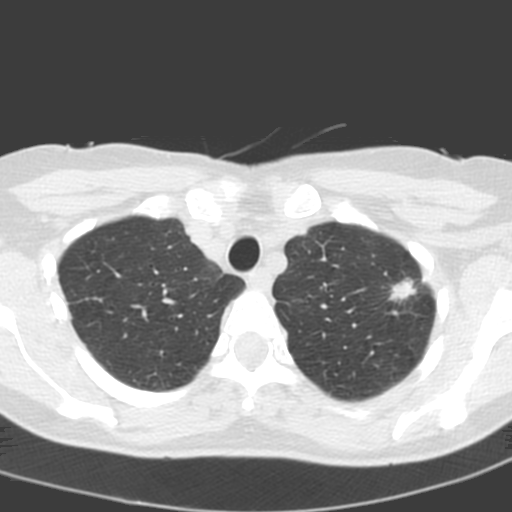
Low-dose screening chest CT, one axial slice; slice 160 of 193 in the series (ordered by position); 120 kVp; lung window (W 1500 / L -600 HU); 512 × 512 image matrix.
Outlined on this slice (outlined manually by an expert reader):
- lesion 1 (tumor, upper lobe of left lung): bounding box (x1, y1, x2, y2) in pixels: (389, 278, 417, 301)